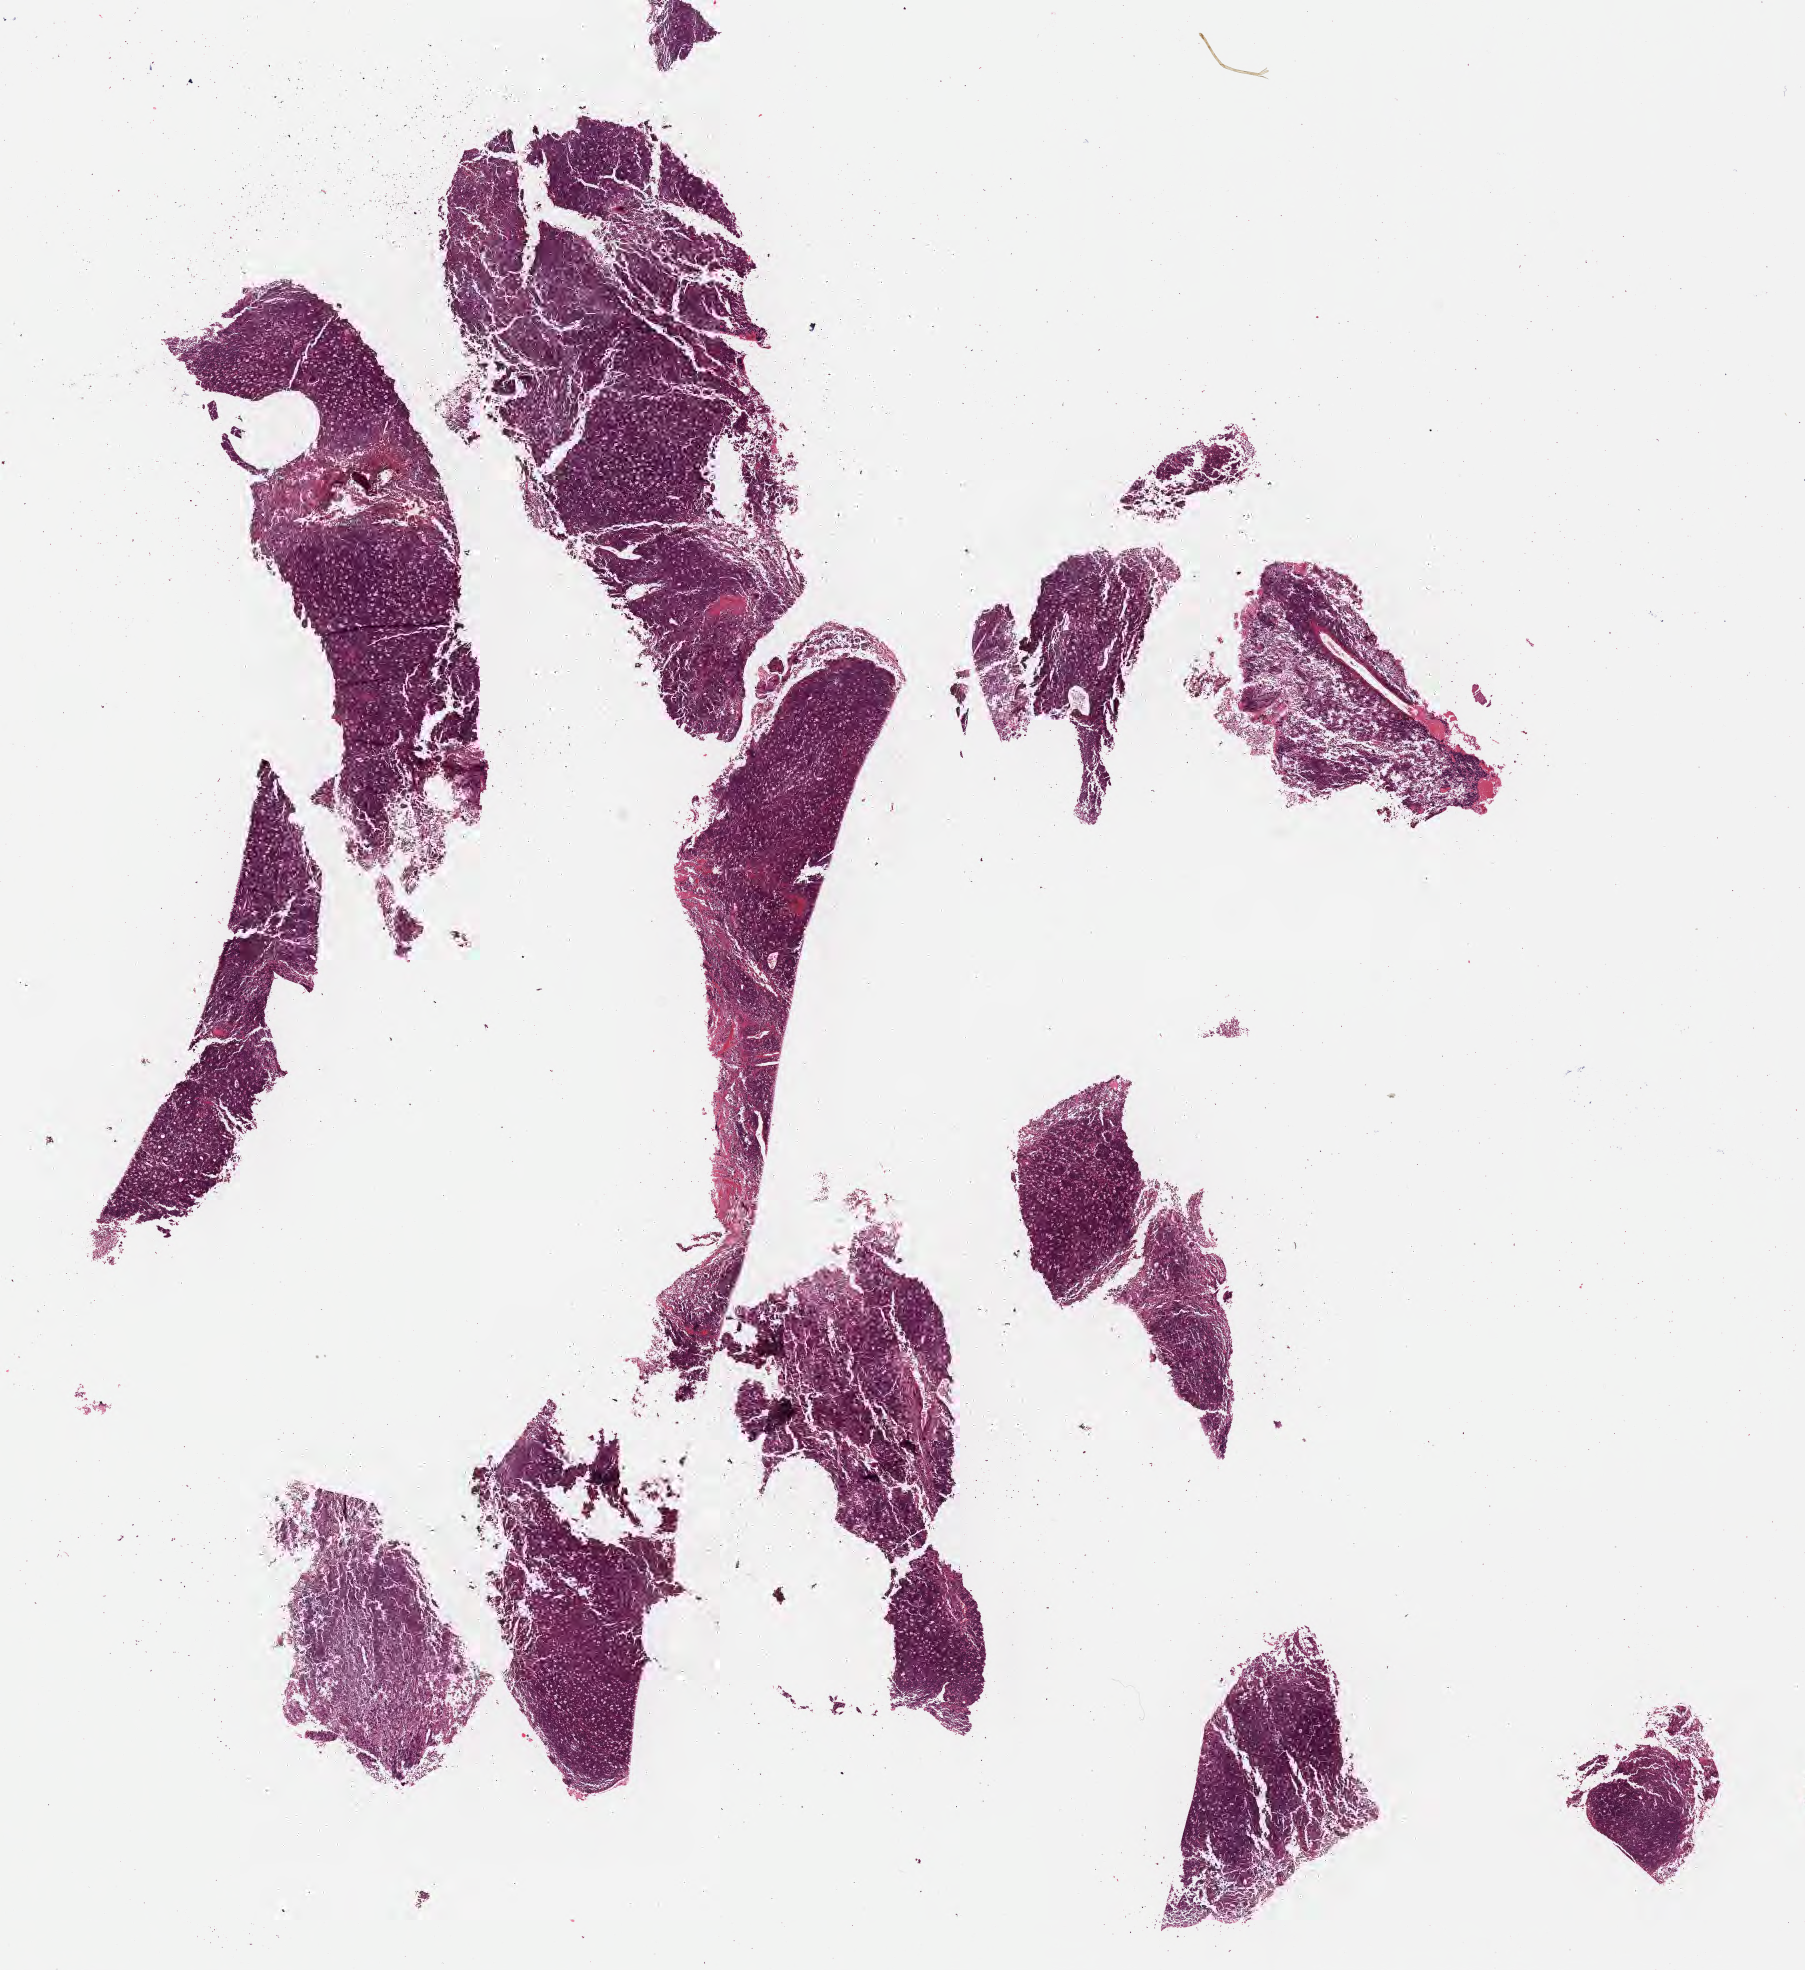
Haematoxylin and eosin whole-slide image — low-resolution overview of the scanned area, about 14.6 x 15.9 mm, FFPE section, specimen: primary tumor. Patient: male, age 11 years. Slide review estimates, as recorded: tumor cells 85%, tumor nuclei 95%, stromal cells 10%, necrosis 5%, normal cells 0%. Infiltration values recorded for this section: lymphocyte infiltration 70%, monocyte infiltration 15%, neutrophil infiltration 0%.
Section: top of the tissue portion. Ann Arbor stage (patient): Stage IV. Histologic diagnosis: Burkitt lymphoma, NOS.